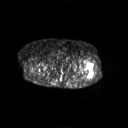
FDG PET of an extremity soft-tissue mass (from a PET/CT study), one axial slice. Slice 255 of 267 in the series (ordered by position). 128 × 128 image matrix. Patient: female, 62 years. Case-level facts recorded for this patient, not image findings: histological type: undifferentiated – high grade; grade: high; site of the primary tumour: left thigh.
Structures marked on this image (expert contour drawn on MRI and transferred to this co-registered scan by the dataset authors):
- gross tumour volume including surrounding oedema: bounding box <86,65,94,78> (left, top, right, bottom; pixels)
- gross tumour volume (mass): <87,72,93,77>